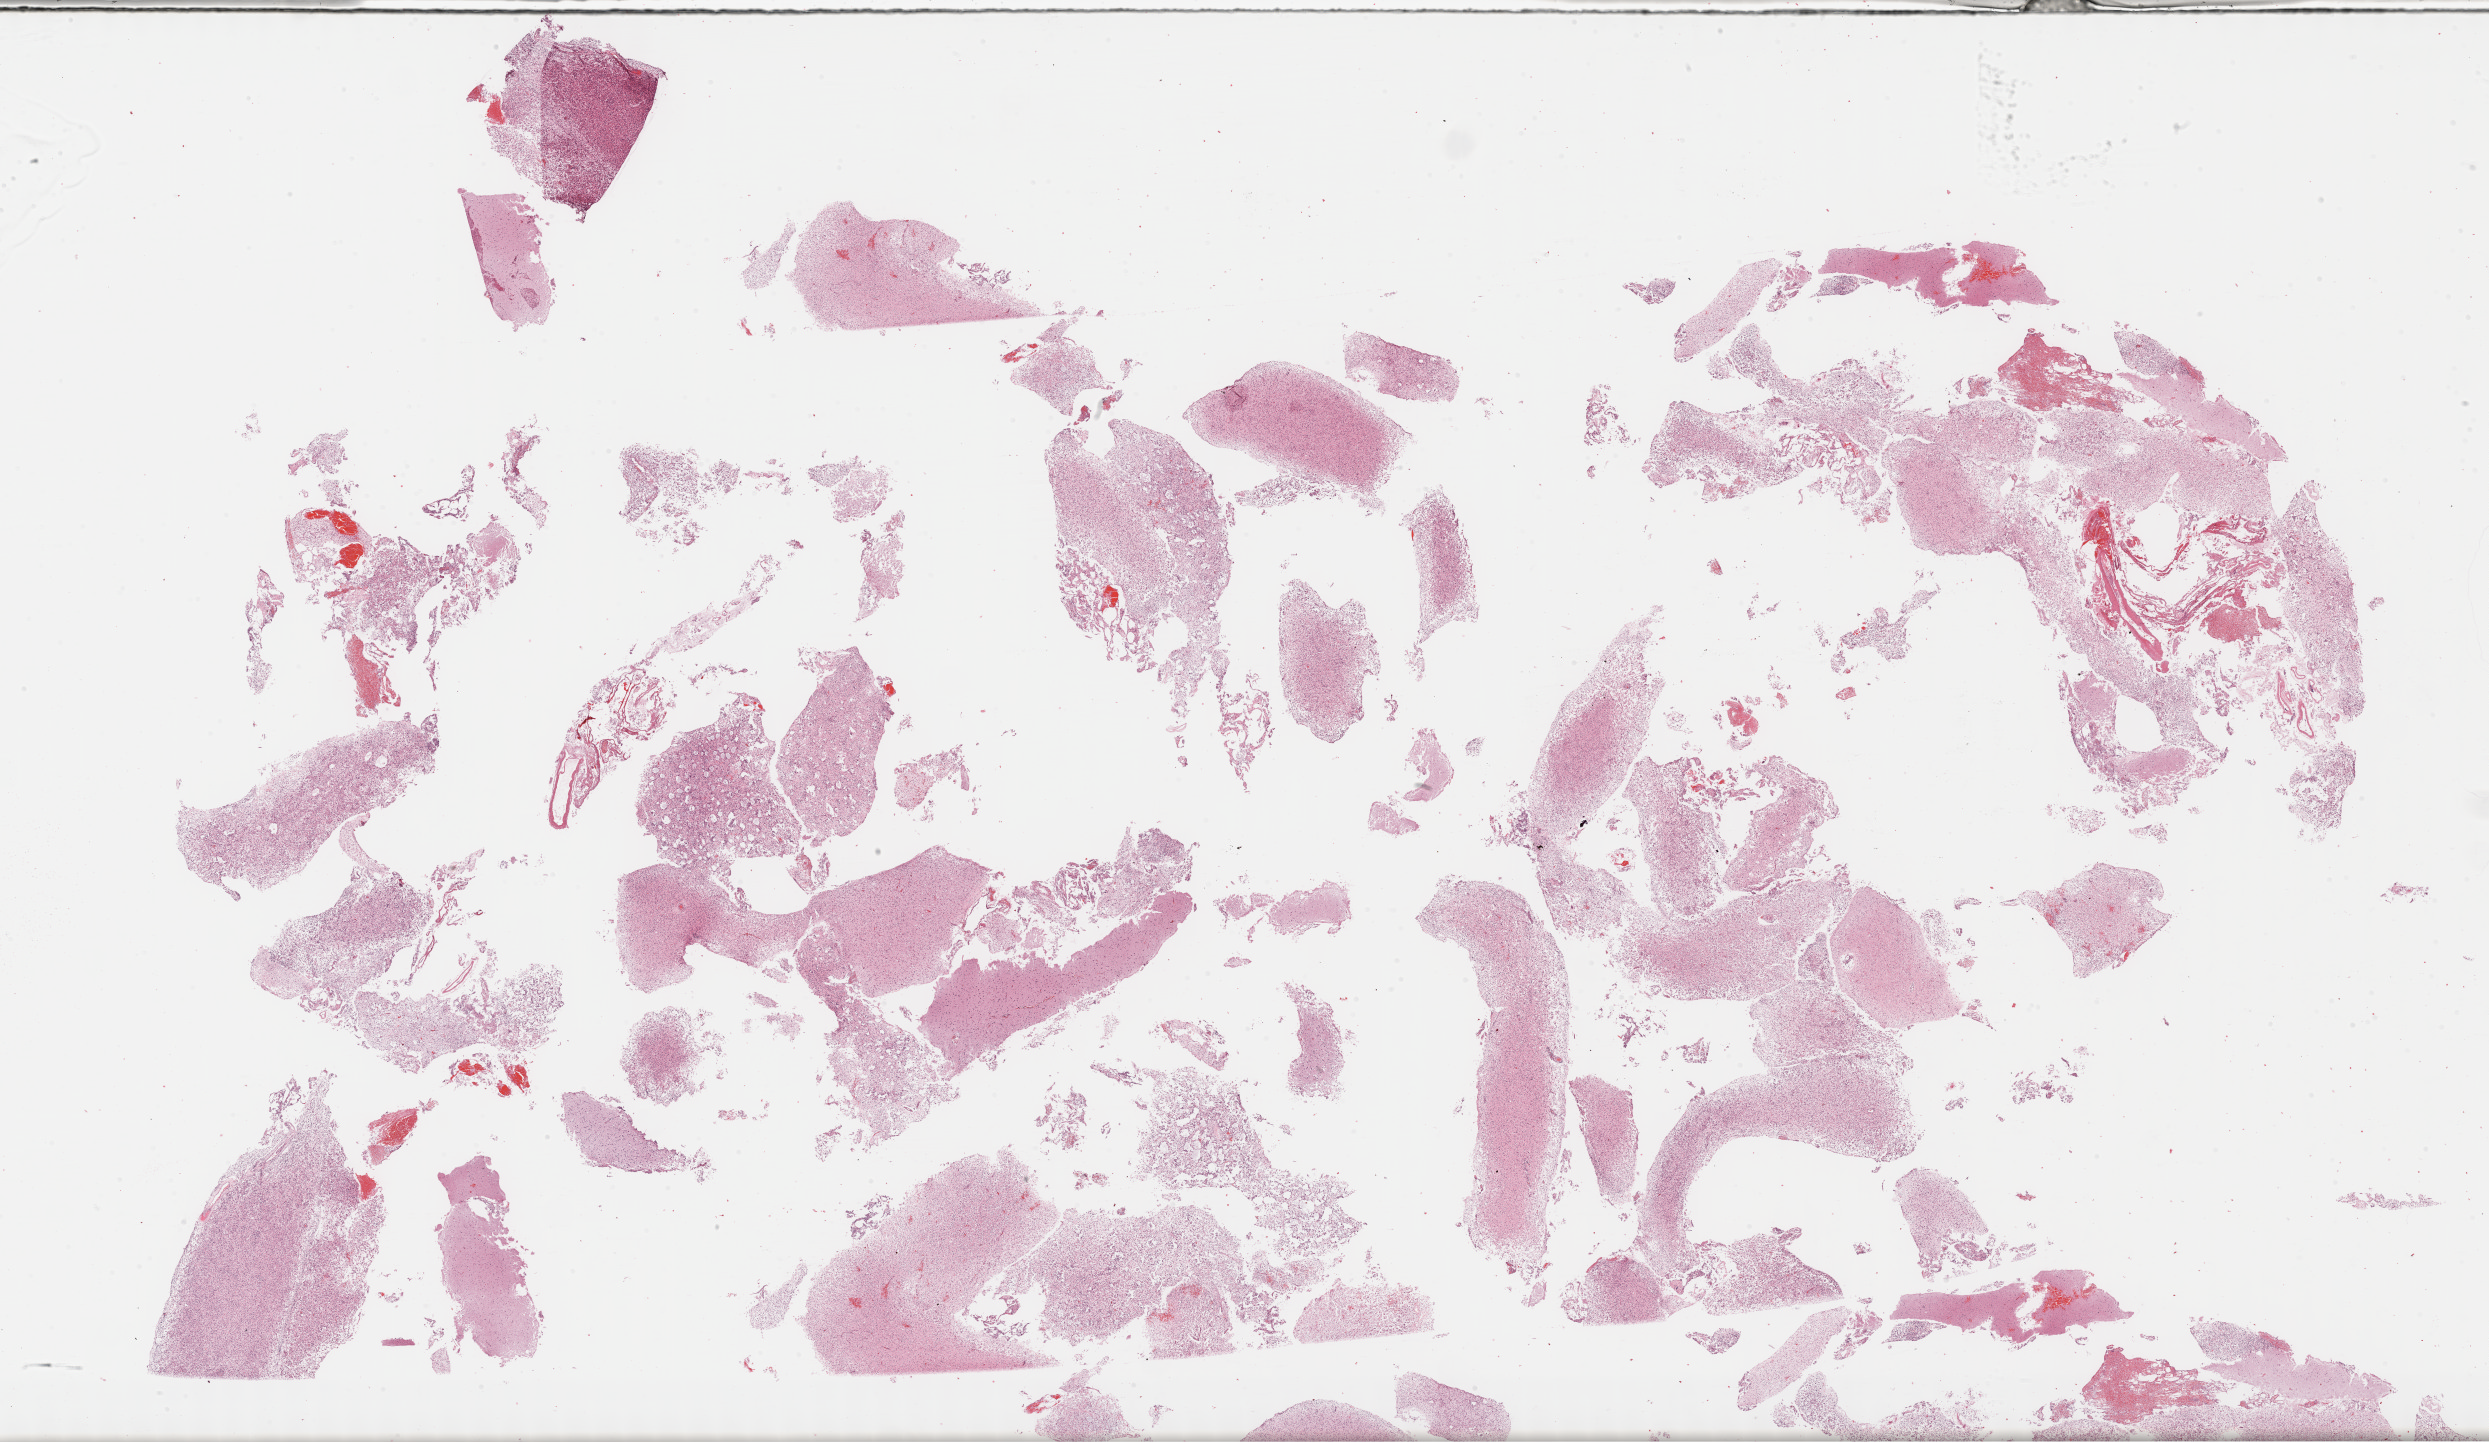
Hematoxylin and eosin (H&E) stained whole-slide image — low-resolution overview of the scanned area, about 40.3 x 23.3 mm (from a 40x scan); FFPE section; brain, primary tumour sample. Patient: male, age at initial diagnosis 31 years. Histologic grade: G2 (moderately differentiated).
Laterality: left. Pathologic diagnosis: Astrocytoma, NOS (cerebrum).